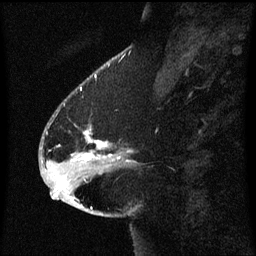
Breast MRI (dynamic contrast-enhanced), one sagittal slice; slice 21 of 60 in the series (ordered by position); dynamic contrast-enhanced series, image 2 of 3 at this slice position (ordered by acquisition); 1.5 T; TE 4.2 ms, TR 8.4 ms; 2 mm slice thickness; 256 × 256 image matrix, field of view 200 × 200 mm. Patient: female, 54 years. Case-level facts recorded for this patient, not image findings: setting: breast cancer imaged before/during neoadjuvant chemotherapy; receptor status: HR-positive, HER2-negative.
Outlined on this slice (semi-automatically segmented with operator editing):
- analysis volume of interest (the breast-tissue region the enhancement analysis was run in; not a lesion): box from (x=46, y=104) to (x=123, y=171) px
- tumour enhancement mask (voxels above the 70 % enhancement threshold inside the analysis volume of interest): (x=85, y=132)–(x=112, y=157)